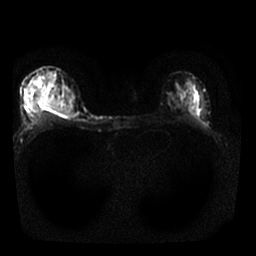
Breast MRI, one axial slice; slice 17 of 25 in the series (ordered by position); diffusion-weighted series; image 2 of 4 stored at this slice position (different b-values; order by instance number); 1.5 T; 4 mm slice thickness; 256 × 256 image matrix, field of view 310 × 310 mm. Female patient.
Structures marked on this image (expert manual segmentation):
- tumour on diffusion-weighted imaging: bounding box (x1, y1, x2, y2) in pixels: (39, 97, 71, 115)